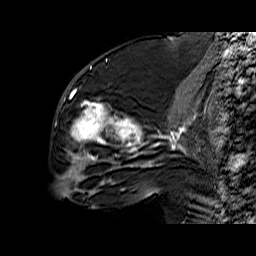
Breast MRI (dynamic contrast-enhanced), one sagittal slice. Position 28 of 60 along the scan axis. Dynamic contrast-enhanced series, time point 2 of 6 at this slice position (early post-contrast). 1.5 T. TE 6.4 ms, TR 32.9 ms. 4 mm slice thickness. 256 × 256 image matrix. Female patient. Case-level facts recorded for this patient, not image findings: setting: breast cancer imaged before/during neoadjuvant chemotherapy; receptor status: triple-negative.
Annotated regions visible in this slice (semi-automatically segmented with operator editing):
- analysis volume of interest (the breast-tissue region the enhancement analysis was run in; not a lesion): box from (x=57, y=65) to (x=159, y=174) px
- tumour enhancement mask (voxels above the 100 % enhancement threshold inside the analysis volume of interest): (x=71, y=91)–(x=159, y=168)